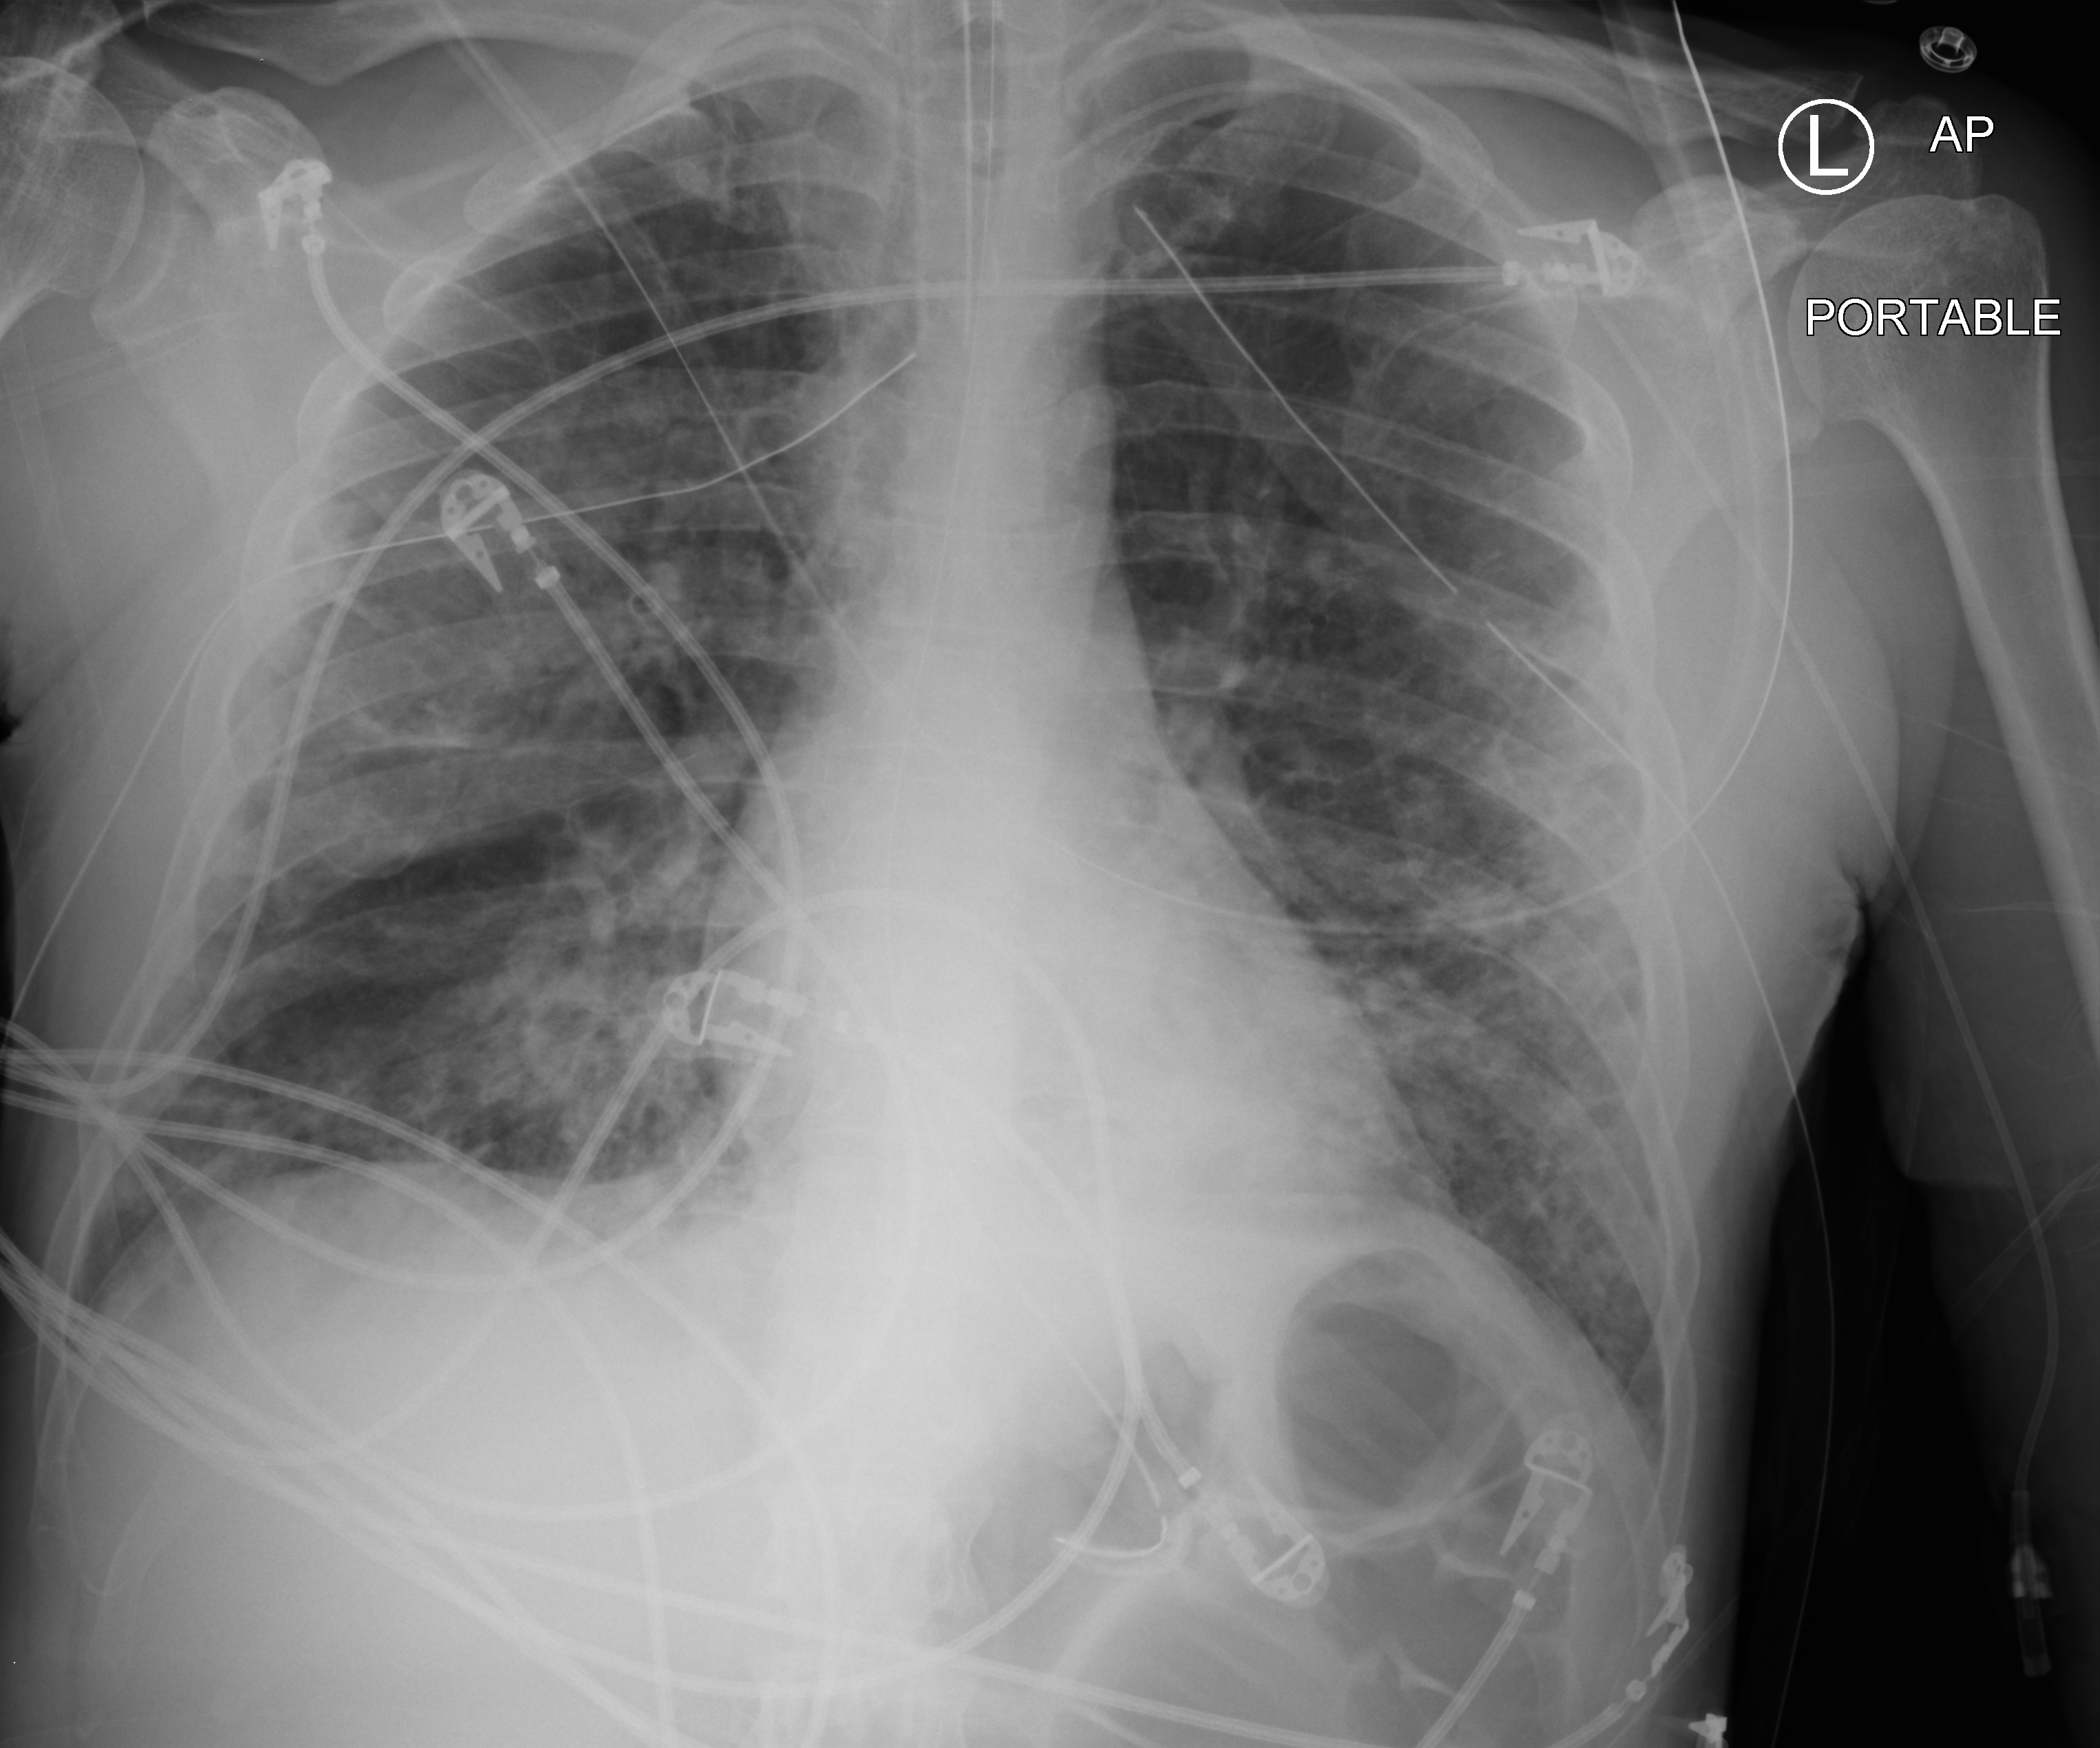
Portable chest radiograph, anteroposterior (AP) projection. Male patient hospitalised with COVID-19, age 18–59 years.
Hospital-stay facts (about this admission, not read from this image; timing relative to this image not recorded): mechanically ventilated during this hospital stay: yes.